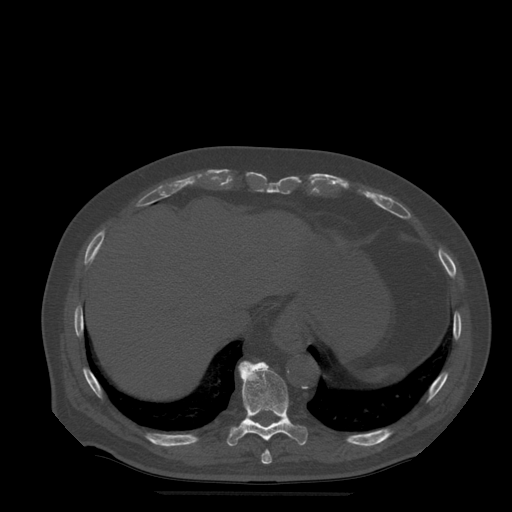
CT including the spine, one axial slice. Slice 267 of 522 in the series (ordered by position). Bone window (W 1800 / L 400 HU). 1.25 mm slice thickness. 512 × 512 image matrix, field of view 420 × 420 mm. Patient age 72 years. Case-level facts recorded for this patient, not image findings: primary cancer: prostate.
Annotated regions visible in this slice (semi-automatic segmentation, software-assisted and operator-edited):
- T10 vertebra: box from (x=227, y=362) to (x=308, y=447) px
- T11 vertebra: (x=243, y=362)–(x=249, y=363)
- T9 vertebra: (x=262, y=450)–(x=272, y=465)